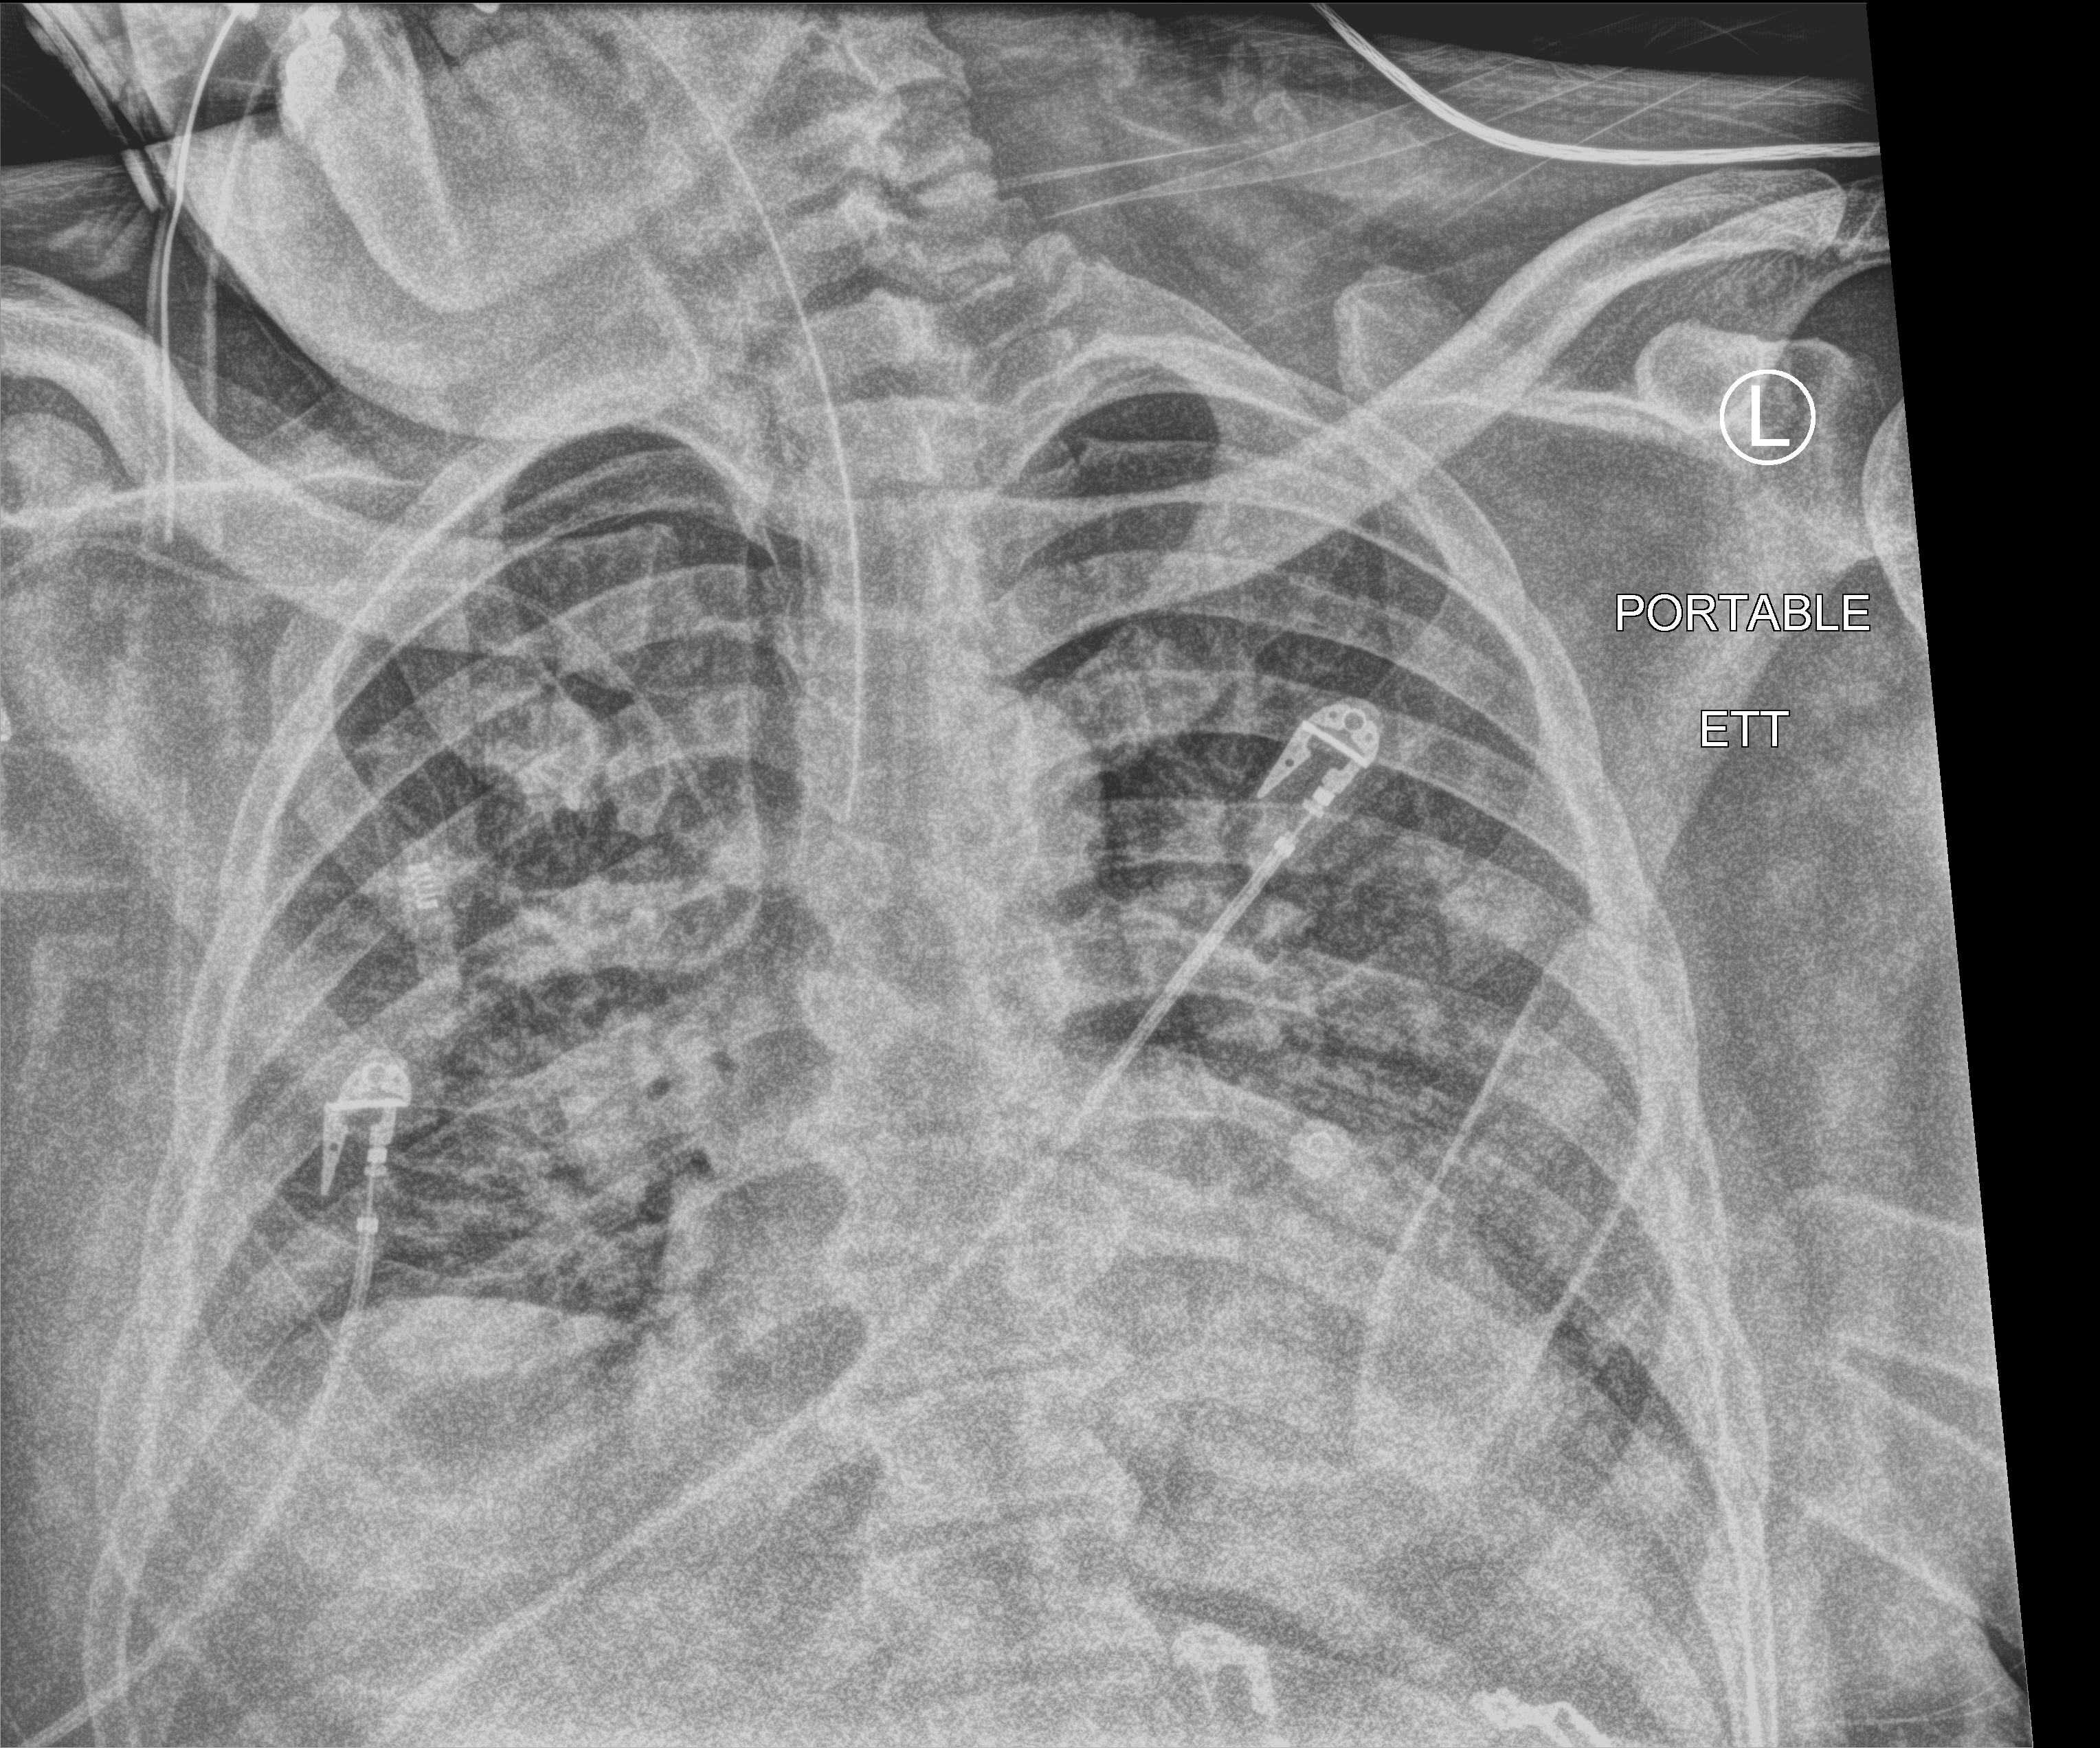
Bedside chest radiograph (computed radiography), anteroposterior (AP) projection. Male patient hospitalised with COVID-19, age 18–59 years.
From the hospital-stay record, not from the radiograph (when in the stay this image was taken is not recorded):
- mechanically ventilated during this hospital stay: yes